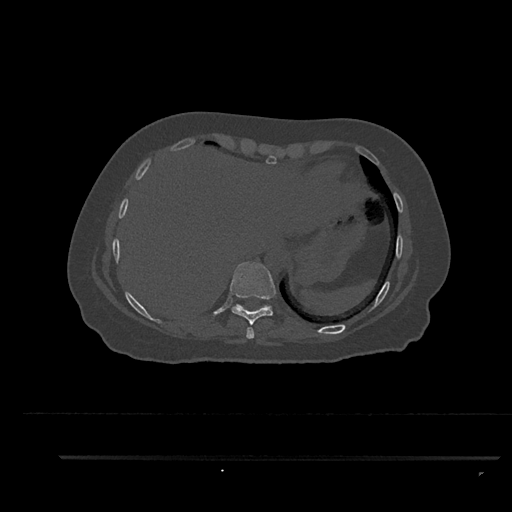
CT including the spine, one axial slice. Slice 406 of 797 in the series (ordered by position). 120 kVp. Bone window (W 1800 / L 400 HU). 0.5 mm slice thickness. 512 × 512 image matrix, field of view 408 × 408 mm. Patient: female, 44 years. From the clinical record (not read from this slice): primary cancer: renal; vertebrae with lytic lesions (as recorded): L1.
Annotated regions visible in this slice (semi-automatic segmentation, software-assisted and operator-edited):
- T10 vertebra: bounding box (x1, y1, x2, y2) in pixels: (236, 304, 272, 308)
- T8 vertebra: (246, 327, 255, 339)
- T9 vertebra: (230, 261, 276, 326)